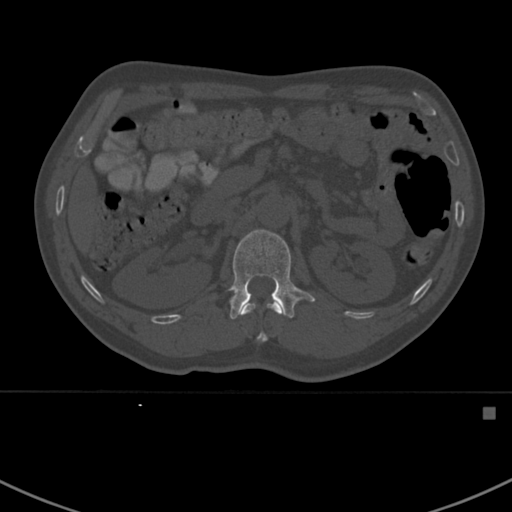
CT including the spine, one axial slice; slice 314 of 412 in the series (ordered by position); reconstruction kernel Br40s; 120 kVp; bone window (W 1800 / L 400 HU); 1.5 mm slice thickness; 512 × 512 image matrix, field of view 358 × 358 mm. Male patient, age 59 years. From the clinical record (not read from this slice): primary cancer: prostate.
Outlined on this slice (semi-automatic segmentation, software-assisted and operator-edited):
- L1 vertebra: bounding box <209,229,315,319> (left, top, right, bottom; pixels)
- T12 vertebra: <241,303,281,342>